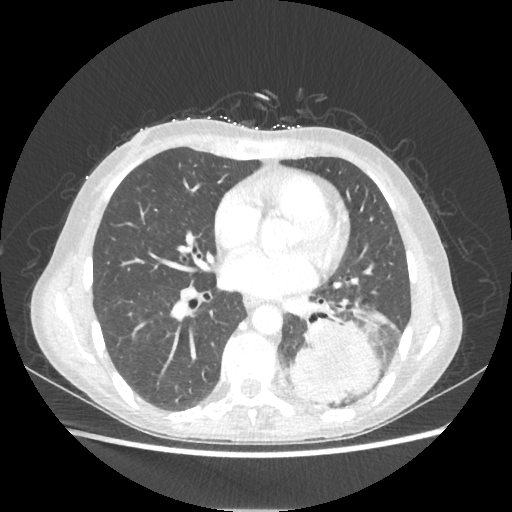
Chest CT, one axial slice; slice 99 of 221 in the series (ordered by position); reconstruction kernel STANDARD; lung window (W 1500 / L -600 HU); 1.25 mm slice thickness; 512 × 512 image matrix, field of view 360 × 360 mm. Patient: female, 53 years. From the clinical record (not read from this slice): clinical TNM (as recorded): T3 N0 M0.
Annotated regions visible in this slice (rectangle marked by the reading radiologist):
- lung tumour (recorded histology: adenocarcinoma): box from (x=286, y=320) to (x=379, y=403) px